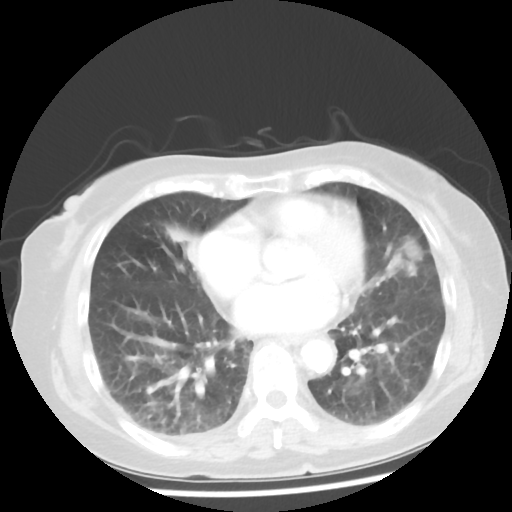
Chest CT, one axial slice; slice 18 of 50 in the series (ordered by position); reconstruction kernel STANDARD; 100 kVp; lung window (W 1500 / L -600 HU); 5 mm slice thickness; 512 × 512 image matrix, field of view 332 × 332 mm. Female patient, age 77 years. Case-level facts recorded for this patient, not image findings: clinical TNM (as recorded): T2 N3 M1a.
Structures marked on this image (rectangle marked by the reading radiologist):
- lung tumour (recorded histology: adenocarcinoma): bounding box <386,228,425,282> (left, top, right, bottom; pixels)